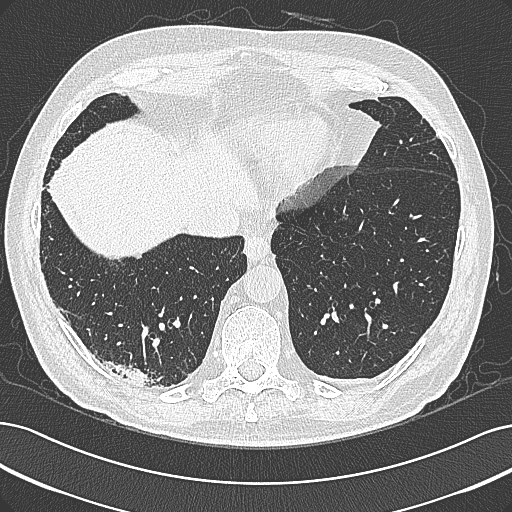
Chest CT (low-dose screening protocol), one axial image; baseline screening round; lung window (W 1500 / L -600 HU); 1 mm slice thickness; lung (sharp) reconstruction kernel (B80f); slice 226 of 355 in the series. Male, age 68 years at enrolment. Former smoker at enrolment.
Lesion marked by an expert reader, bounding box <97,341,183,403> (left, top, right, bottom; pixels). Screening reader's record for this exam: no non-calcified nodule ≥4 mm recorded. Later outcome: lung cancer diagnosed 154 days after this screen — mucinous adenocarcinoma, right lower lobe, well differentiated (G1), stage IB (AJCC 6th edition), 50 mm at pathology.